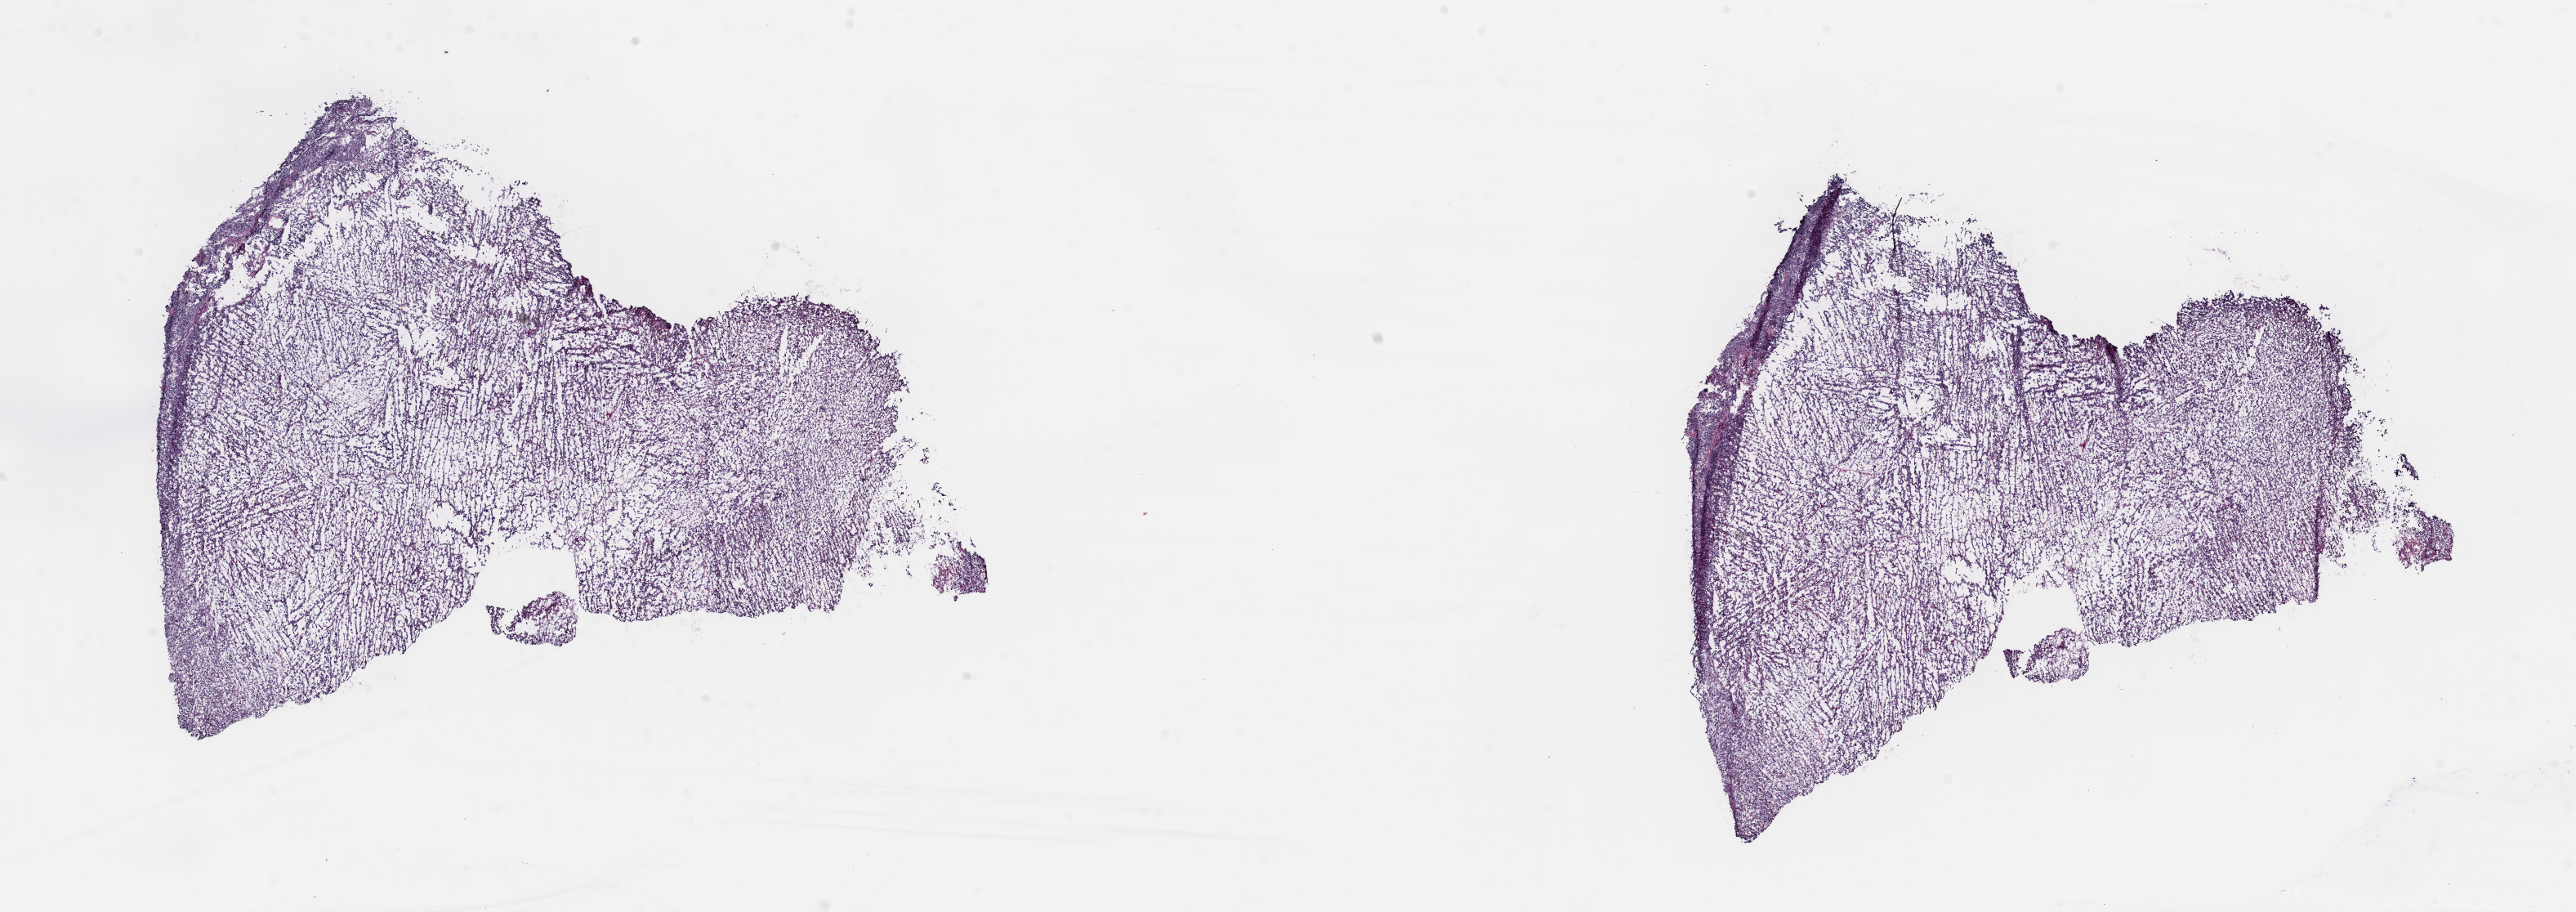
Digitized H&E-stained tissue section (whole slide) — shown as a low-resolution overview of the whole scanned area (about 24.9 x 8.8 mm); frozen section from the top of the tissue portion; primary tumour sample from the uterus. Female, age 63 years at initial diagnosis. Slide review estimates, as recorded: tumour cells 90%, tumour nuclei 90%, normal cells 0%, stromal cells 0%, necrosis 10%. Infiltration values recorded for this section: lymphocyte infiltration 0%, monocyte infiltration 0%, neutrophil infiltration 0%.
Histologic diagnosis: Mullerian mixed tumor. FIGO stage: IIIC2.